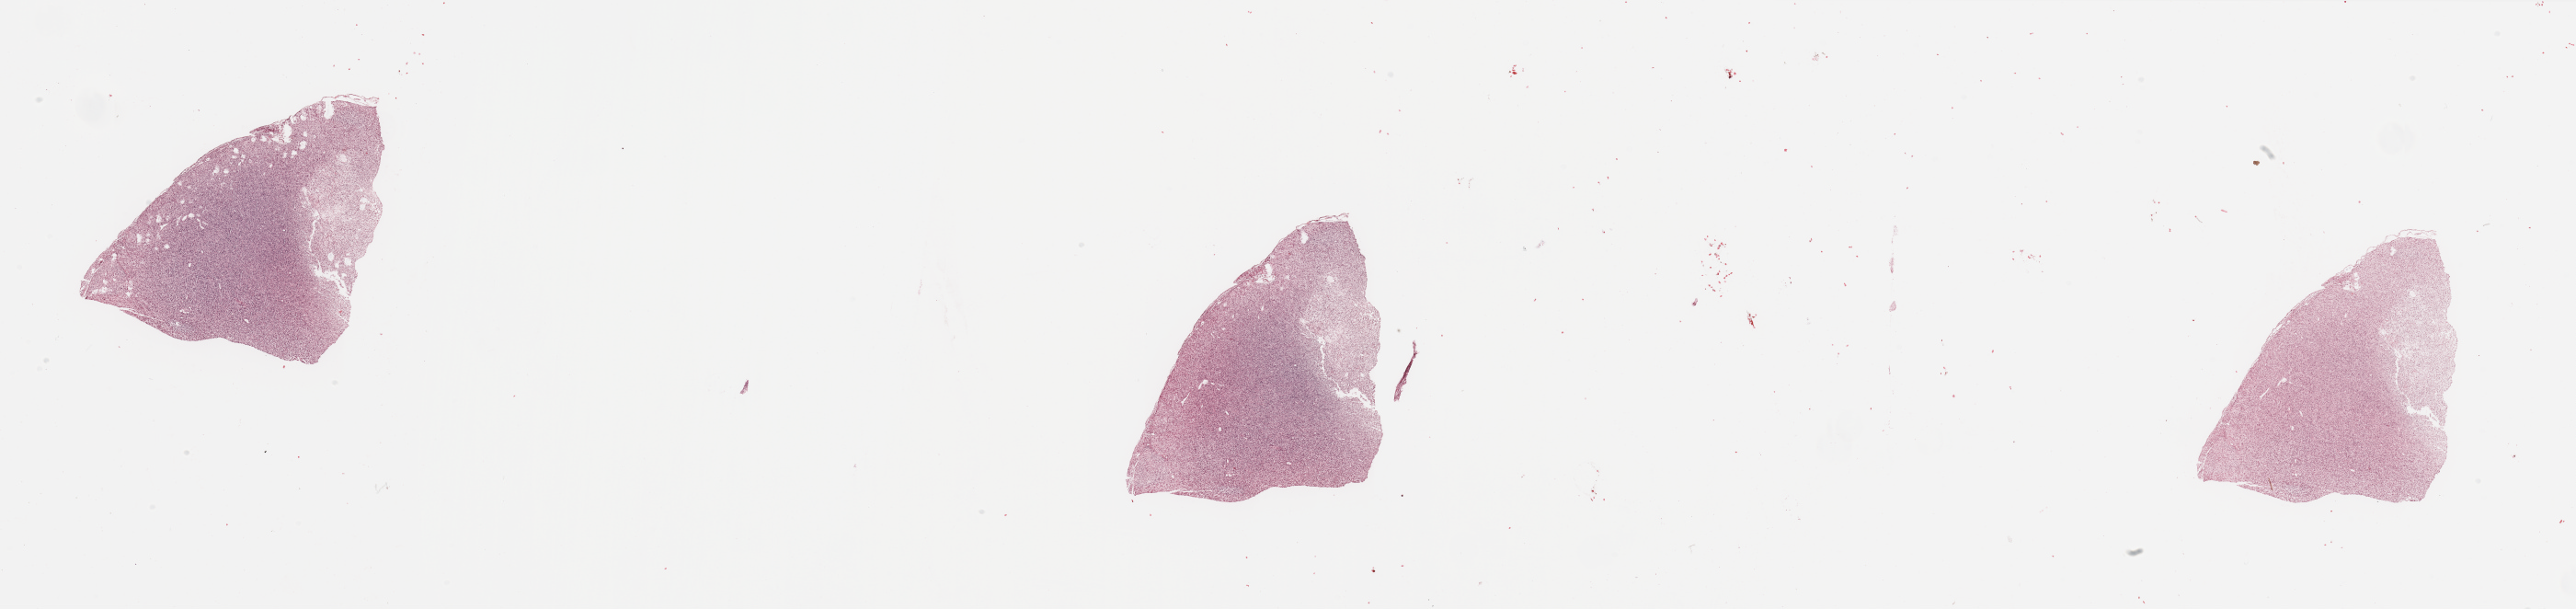
Digitized H&E tissue section (whole slide), shown as a low-resolution overview of the whole scanned area (about 44.3 x 10.5 mm); tumour tissue sample, brain. Male, 70 y/o.
Primary tumour site (as recorded): frontal lobe. Histologic diagnosis: Glioblastoma.